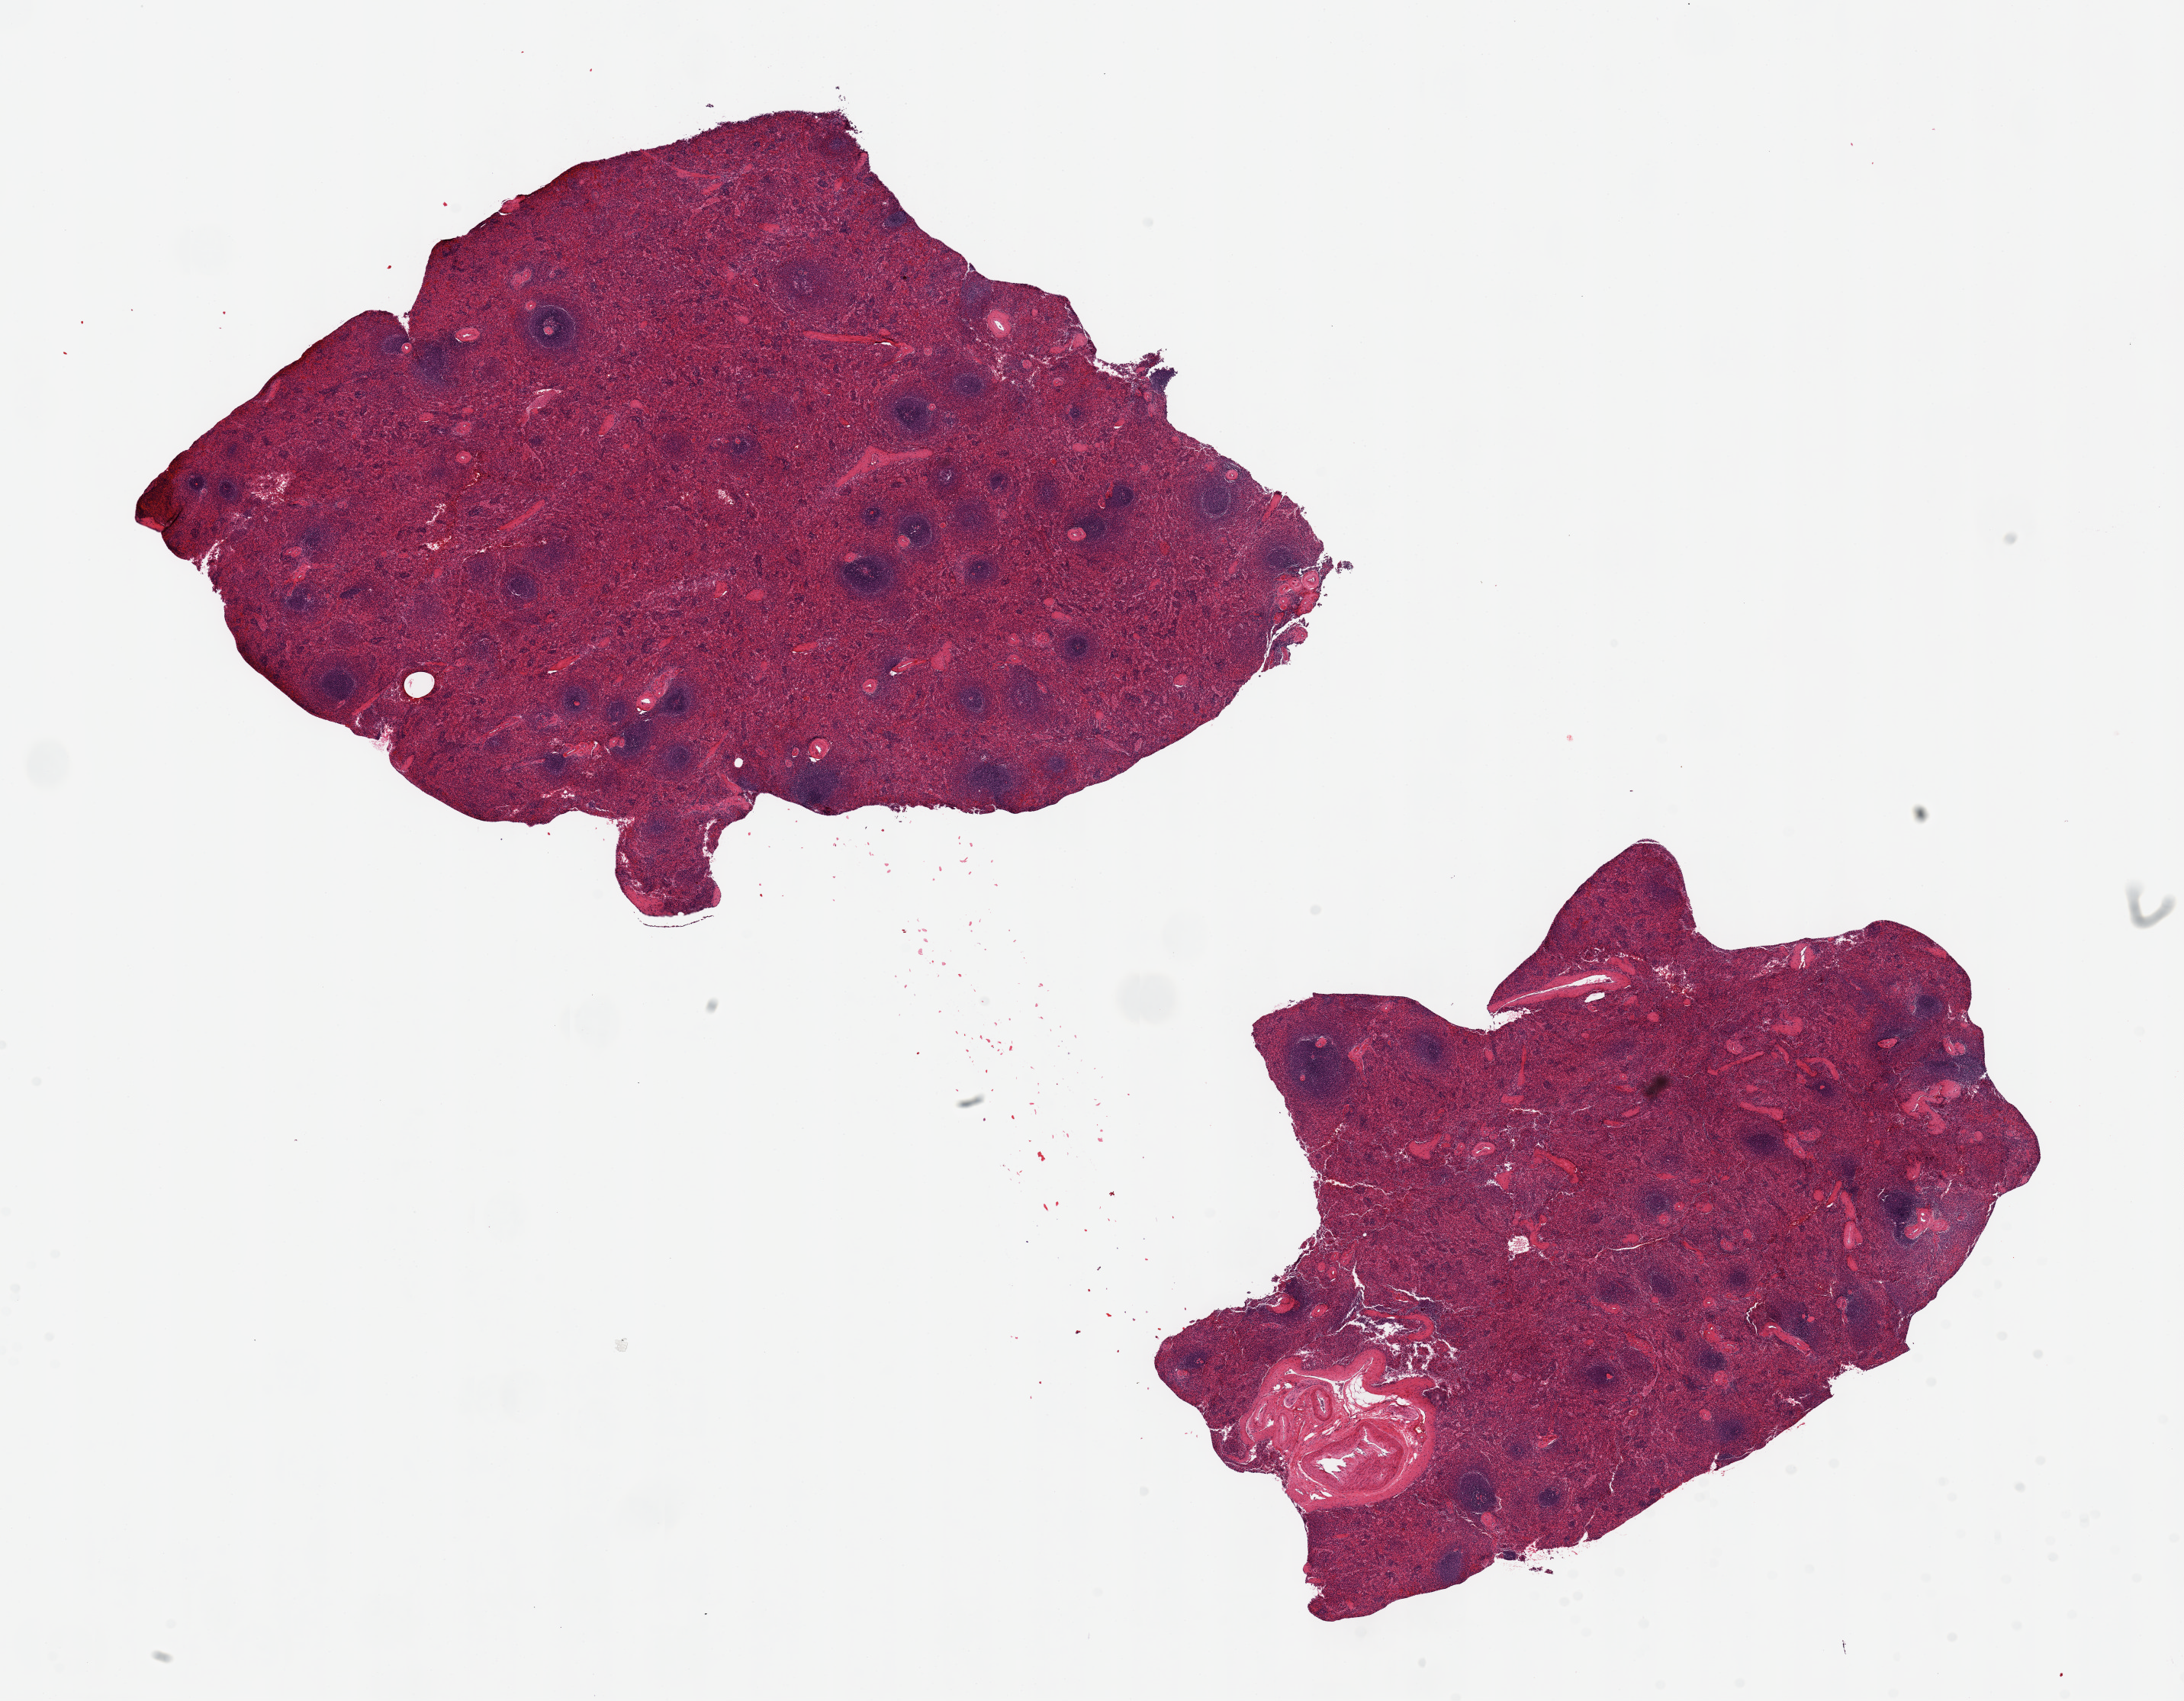
Hematoxylin and eosin (H&E) whole-slide image, brightfield, a low-resolution overview of the entire scanned area, about 22.6 x 17.6 mm; PAXgene-fixed, paraffin-embedded tissue; target tissue: spleen; tissue donor sample. Donor sex: female.
Pathologist's review note for this sample: 2 pieces ~8x7 mm.